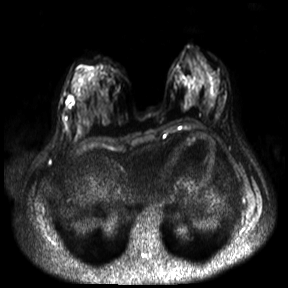
Breast MRI, one axial slice. Slice 12 of 30 in the series (ordered by position). Diffusion-weighted series; image 2 of 4 stored at this slice position (different b-values; order by instance number). 3 T. 4 mm slice thickness. 288 × 288 image matrix. Female patient.
Outlined on this slice (expert manual segmentation):
- tumour on diffusion-weighted imaging: bounding box (x1, y1, x2, y2) in pixels: (71, 96, 73, 99)